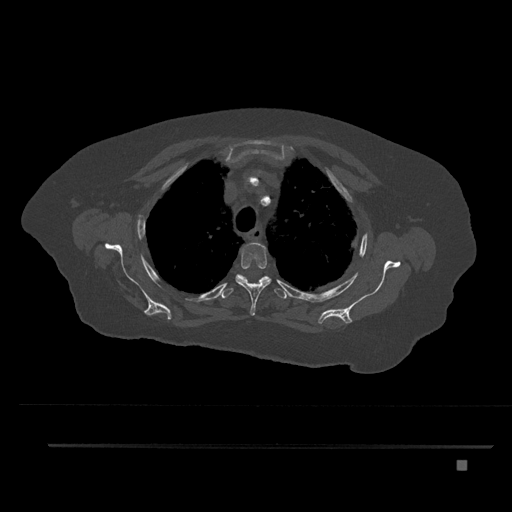
CT including the spine, one axial slice. Position 628 of 797 along the scan axis. Reconstruction kernel Br40s/3. 120 kVp. Bone window (W 1800 / L 400 HU). 0.5 mm slice thickness. 512 × 512 image matrix, field of view 437 × 437 mm. Patient: female, 76 years. Case-level facts recorded for this patient, not image findings: primary cancer: lung; vertebrae with lytic lesions (as recorded): T11, L3.
Outlined on this slice (semi-automatic segmentation, software-assisted and operator-edited):
- T3 vertebra: bounding box [x1, y1, x2, y2] px = [235, 242, 271, 316]
- T4 vertebra: [219, 274, 287, 299]